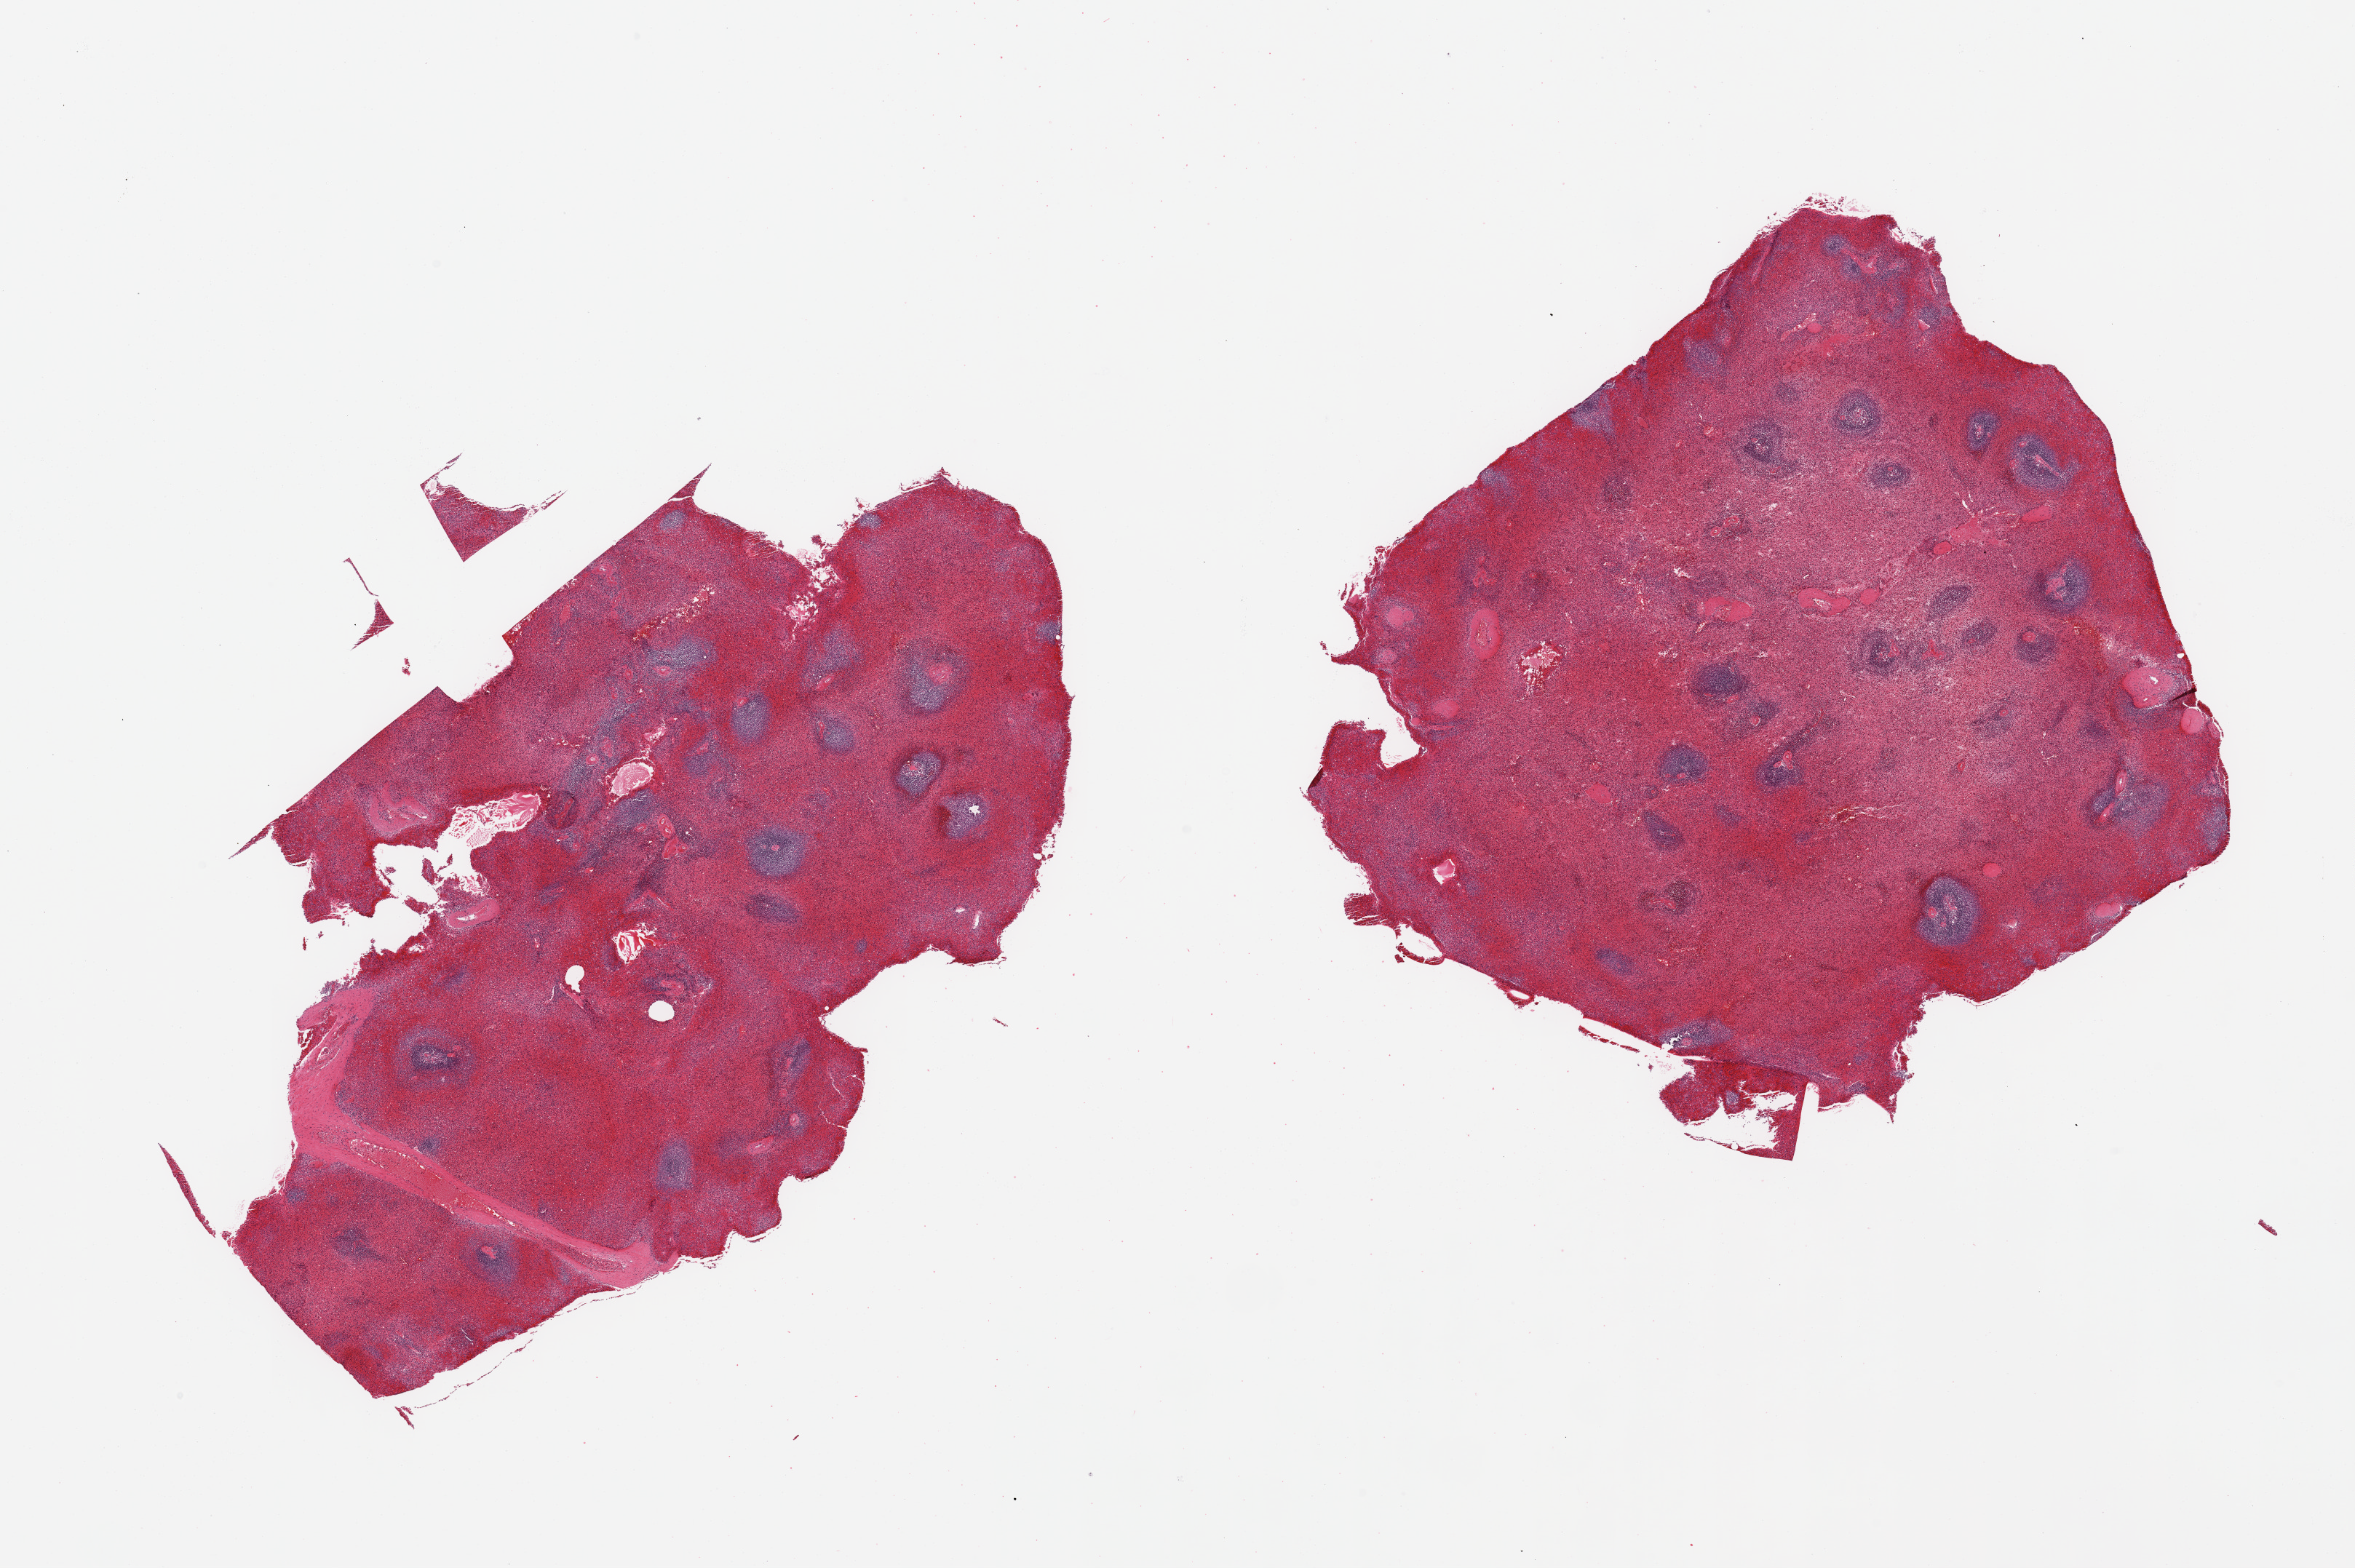
Digitized H&E-stained section, whole scanned area (about 25.6 x 17.0 mm, acquisition: 20x scan) shown as a low-resolution overview; PAXgene-fixed, paraffin-embedded tissue; section of spleen (target tissue); donor tissue sample. Donor sex: male.
Reviewer comment on this tissue sample: 2 pieces, moderate congestion.